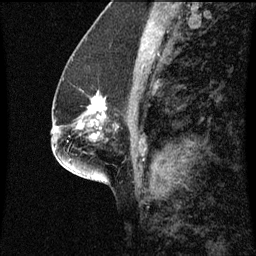
Breast MRI (dynamic contrast-enhanced), one sagittal slice. Position 28 of 60 along the scan axis. Dynamic contrast-enhanced series, image 2 of 3 at this slice position (ordered by acquisition). 1.5 T. TE 4.2 ms, TR 8.9 ms. 2 mm slice thickness. 256 × 256 image matrix. Female patient, age 57 years. Case-level facts recorded for this patient, not image findings: setting: breast cancer imaged before/during neoadjuvant chemotherapy; receptor status: HR-positive, HER2-negative.
Outlined on this slice (semi-automatic segmentation, software-assisted and operator-edited):
- analysis volume of interest (the breast-tissue region the enhancement analysis was run in; not a lesion): bounding box <82,92,118,125> (left, top, right, bottom; pixels)
- tumour enhancement mask (voxels above the 70 % enhancement threshold inside the analysis volume of interest): <95,92,105,115>